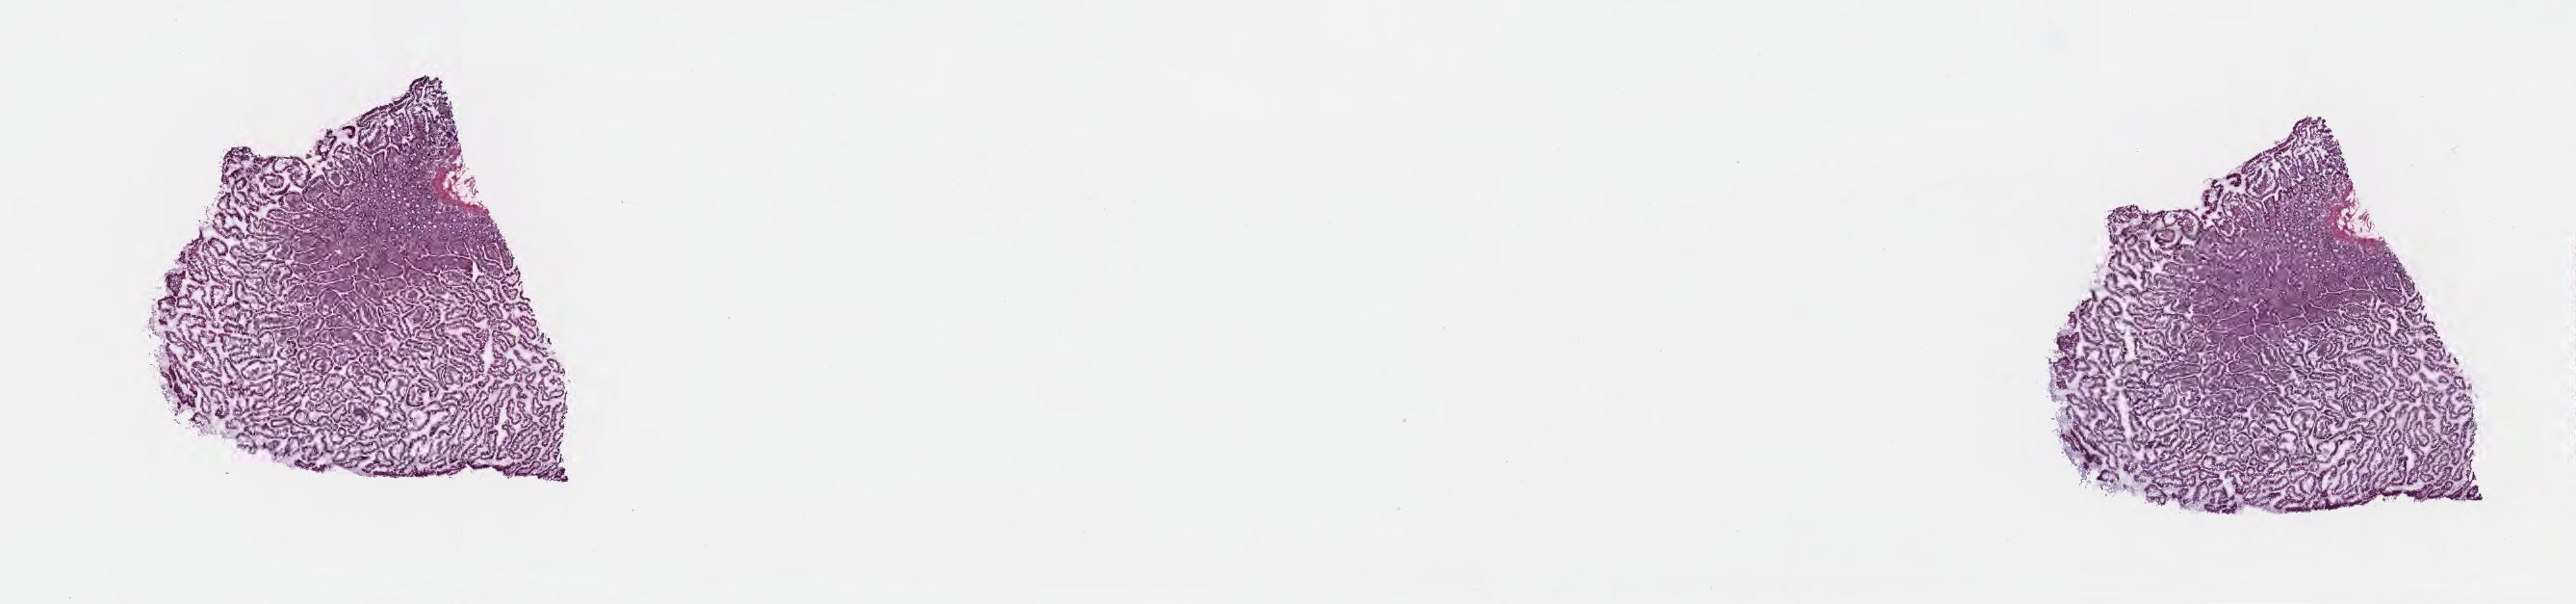
Haematoxylin and eosin whole-slide image, a low-resolution overview of the entire scanned area, about 21.6 x 5.1 mm; frozen section; normal-tissue sample (non-tumor) from a patient with infiltrating duct carcinoma, NOS; anatomic site: head of pancreas. Female patient; age at initial diagnosis 73 years. Pathologist review of this section (percent, as recorded): tumor cells 0%, tumor nuclei 0%, stromal cells 0%, necrosis 0%, normal cells 100%. Infiltration values recorded for this section: lymphocyte infiltration 0%, monocyte infiltration 0%, neutrophil infiltration 0%.
- this section: non-tumor tissue sample; the patient's diagnosis is given above
- section: top of the tissue portion